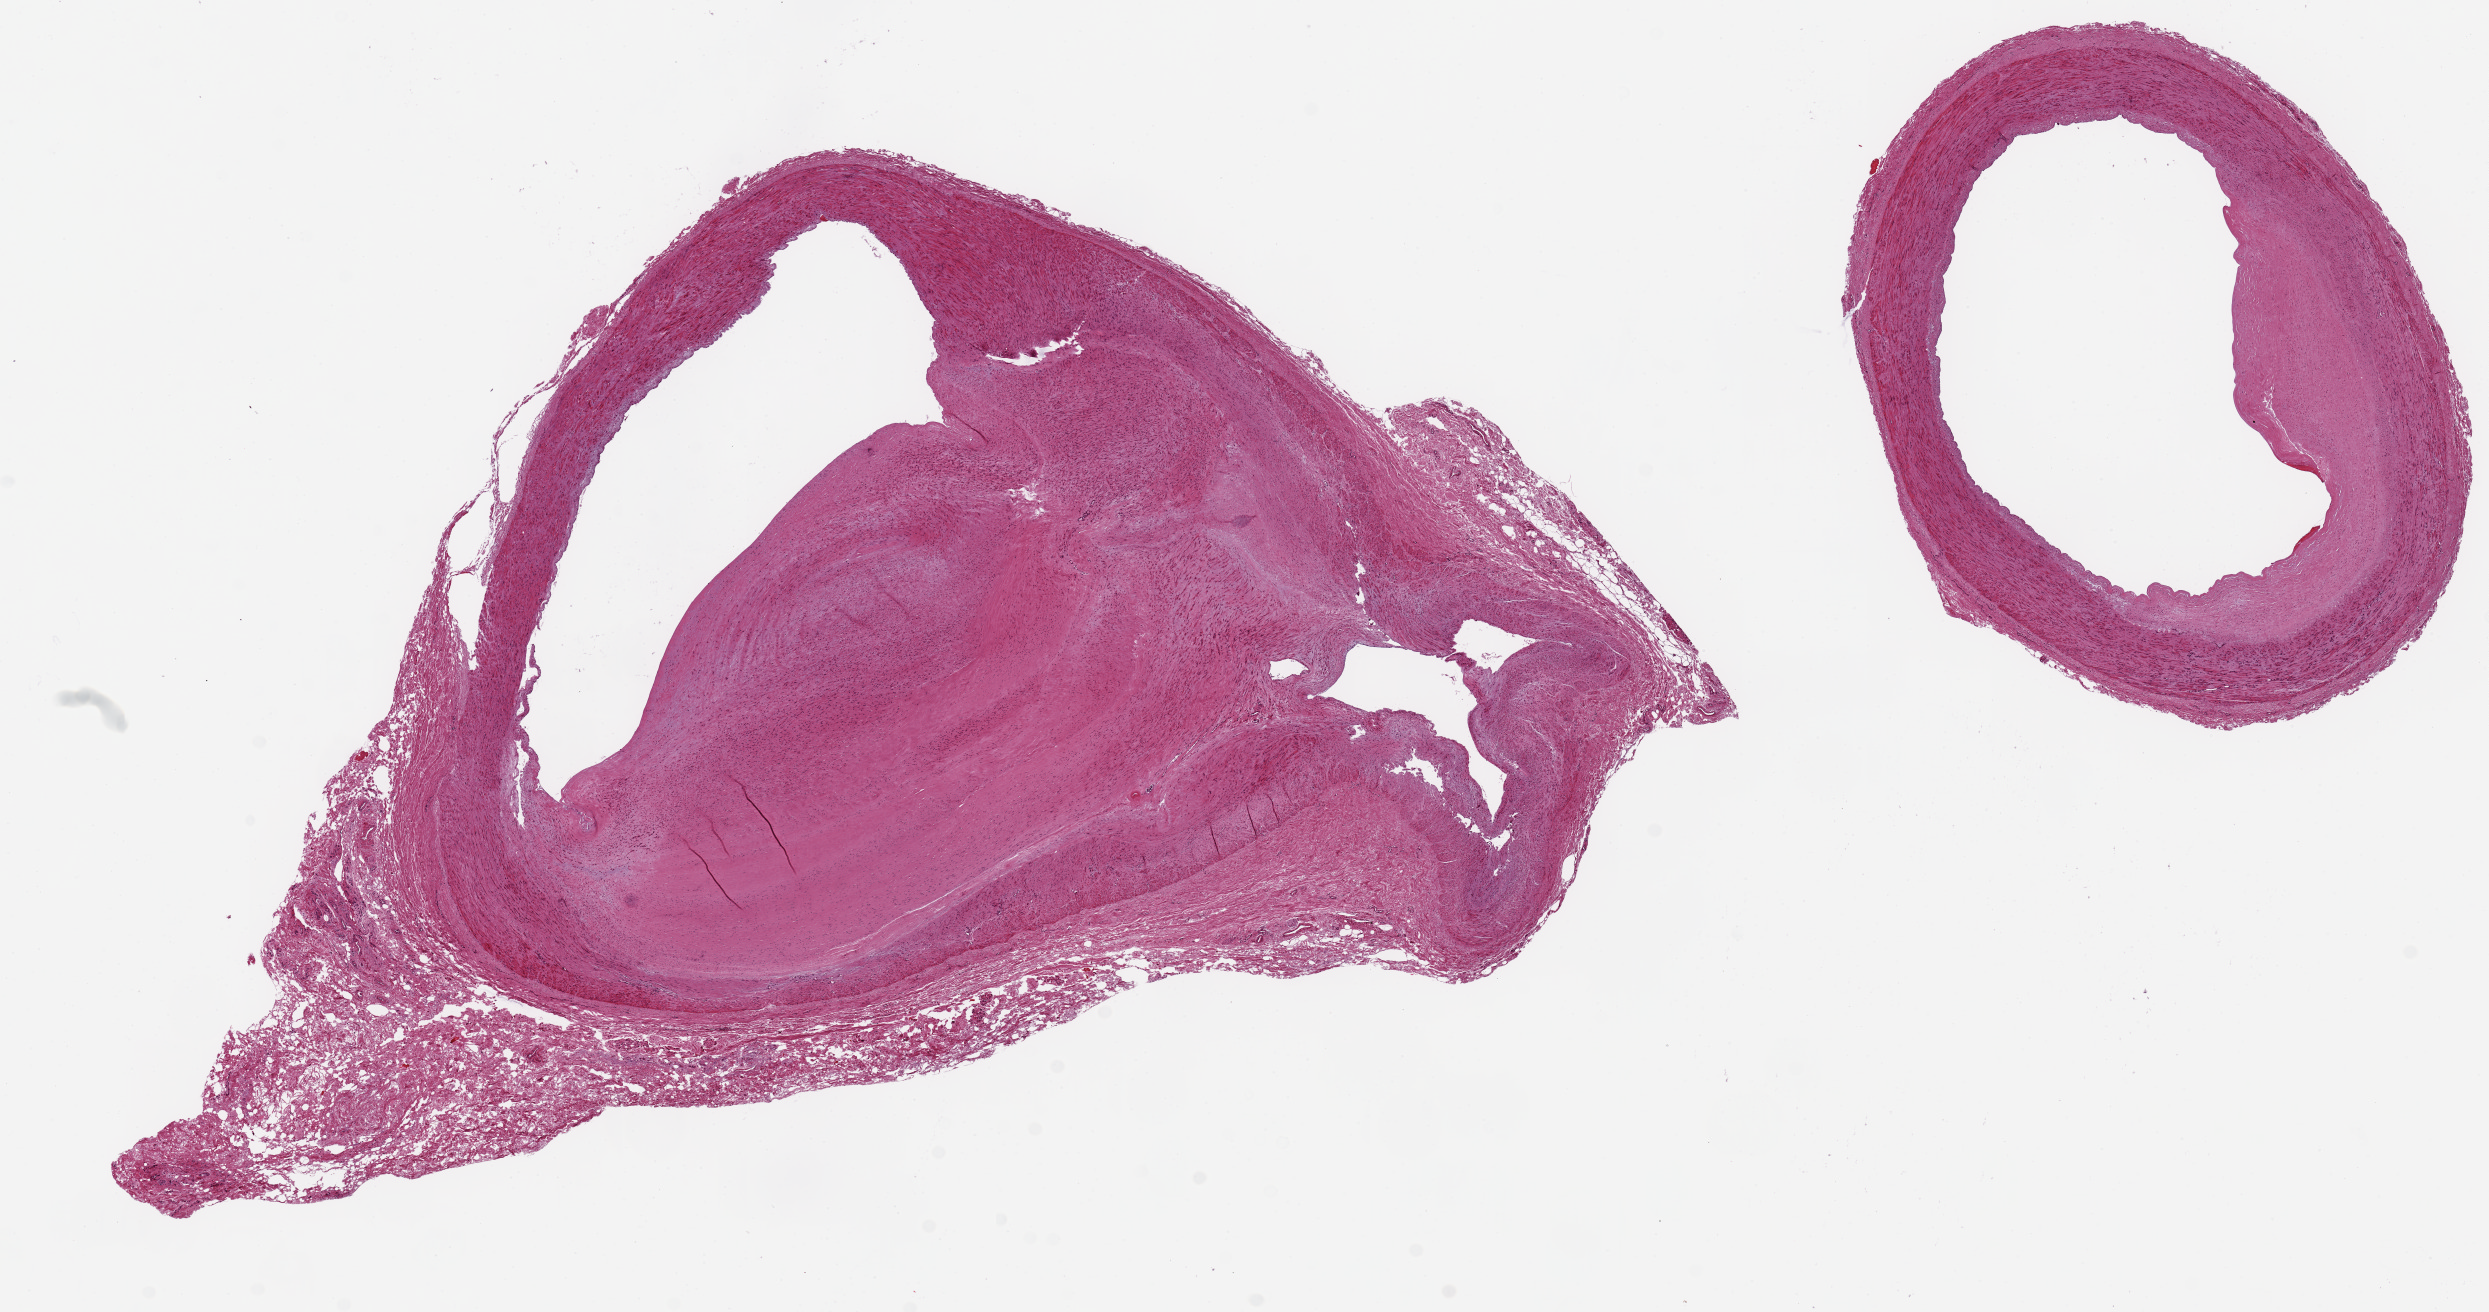
Whole-slide image, haematoxylin and eosin stain, a low-resolution overview of the entire scanned area, about 19.7 x 10.4 mm (acquisition: 20x scan); PAXgene-fixed, paraffin-embedded tissue; target tissue: tibial artery; tissue donor sample. Donor: male.
• reviewer comment on this tissue sample: 2 7x6mm aliquots; prominent peripheral atherosclerosis